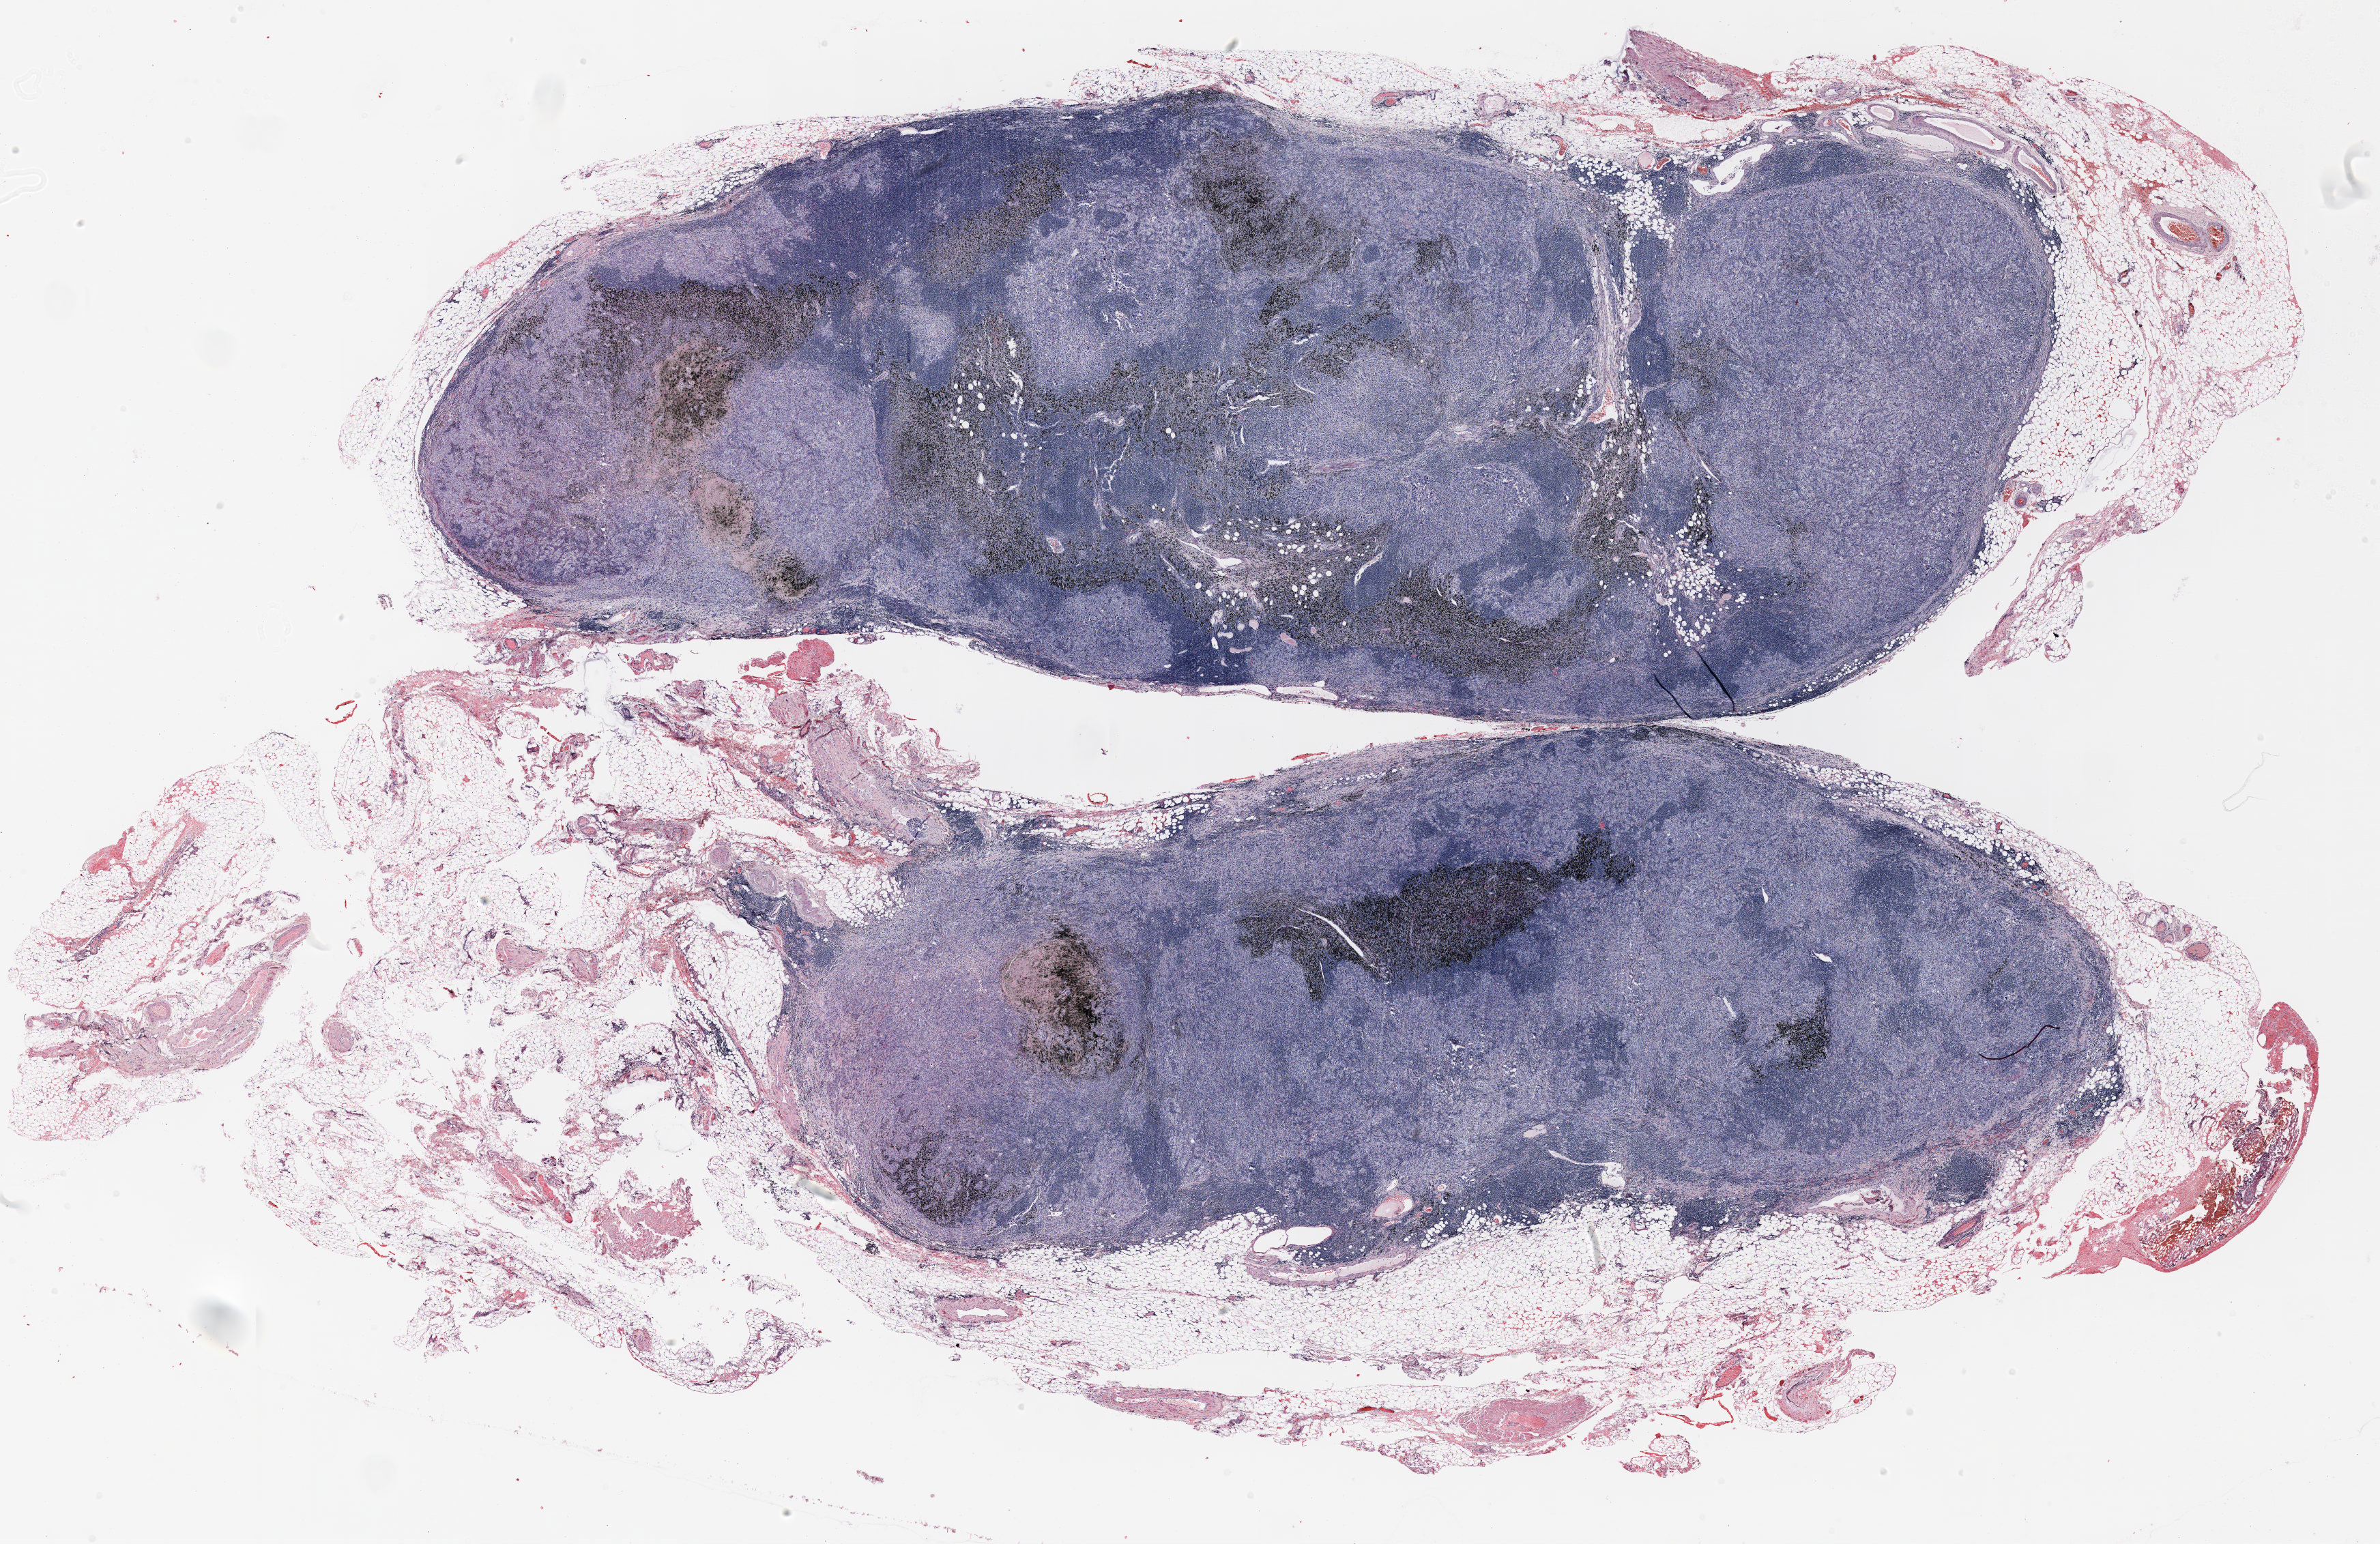
Hematoxylin and eosin (H&E) stained whole-slide image — a low-resolution overview of the entire scanned area, about 28.0 x 18.2 mm (acquisition: 20x scan); FFPE section; lung. Male, age 70 at enrolment. Grade: moderately differentiated (G2).
• ICD-O-3 topography: upper lobe of lung (C34.1)
• primary tumour location (clinical record): left upper lobe
• participant's lung-cancer diagnosis: Adenocarcinoma, NOS
• stage (AJCC 6th edition): IIIA
• tumour size (pathology): 17 mm